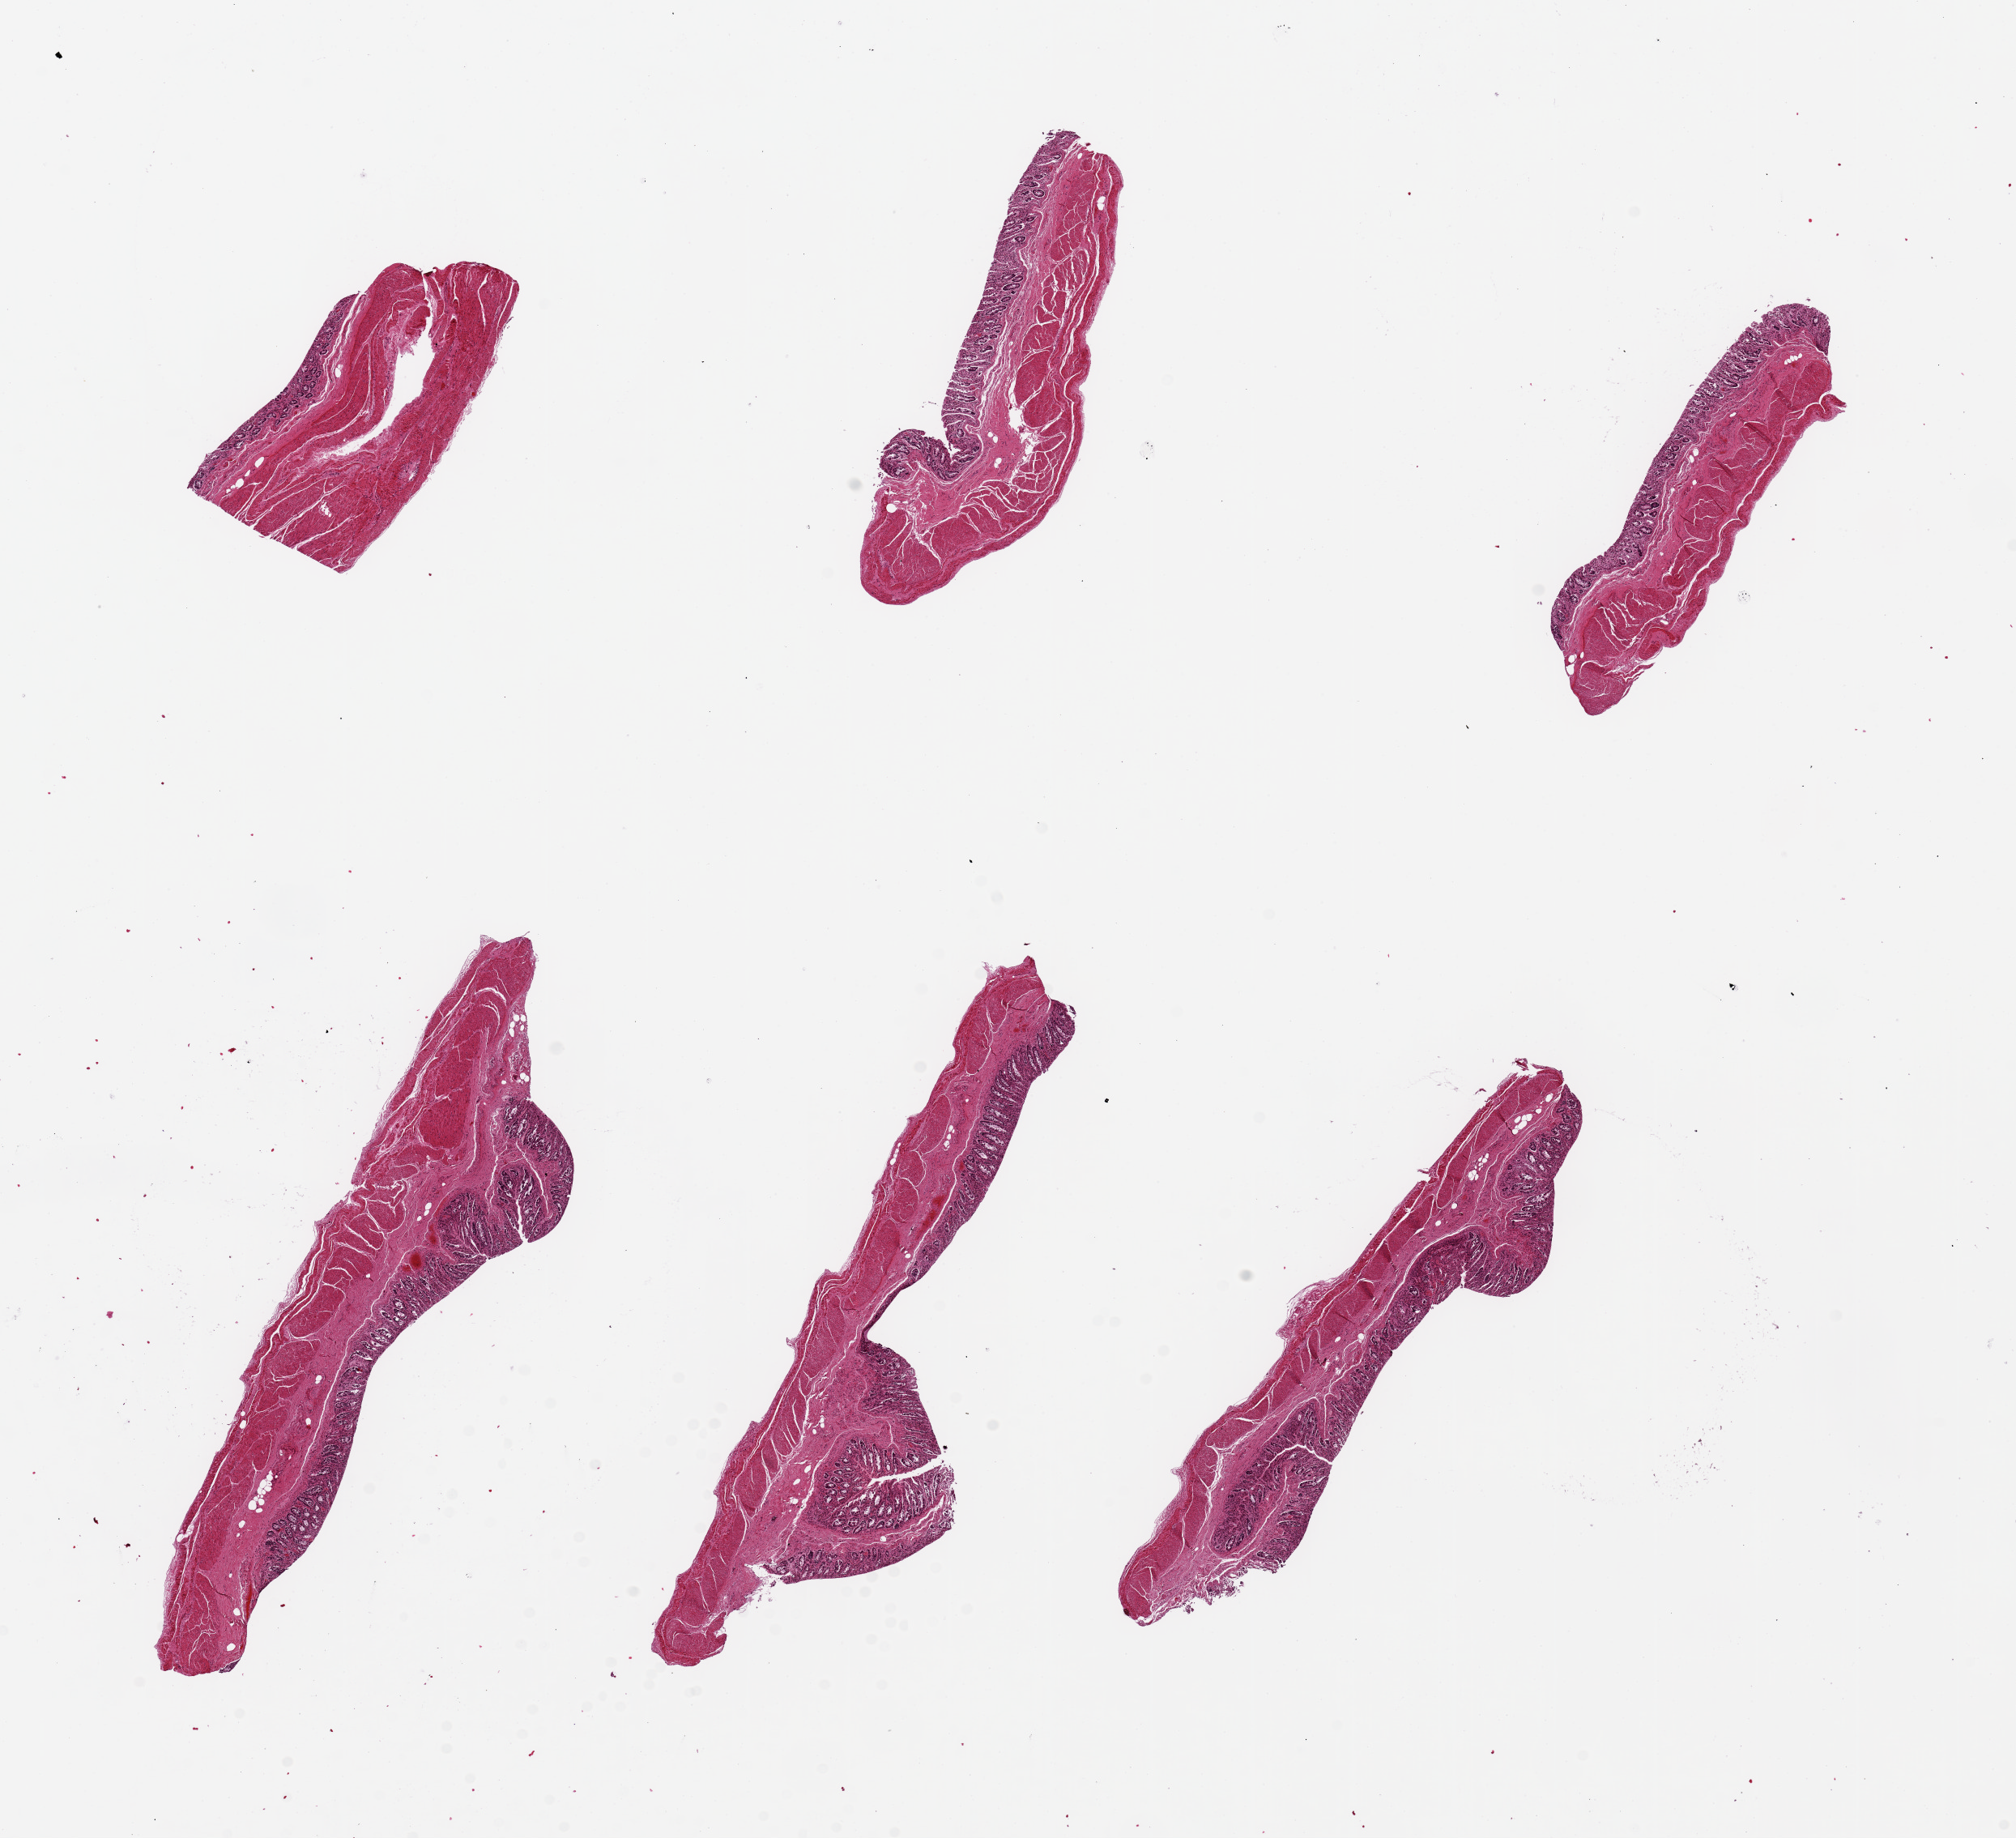
Digitized haematoxylin and eosin-stained section, brightfield — low-resolution overview of the scanned area, about 19.7 x 17.9 mm (slide scanned at 20x), PAXgene-fixed, paraffin-embedded tissue, target tissue: transverse colon, tissue donor sample. Donor: male.
- review note (as recorded): 6 pieces, up to 8x2mm; Well sampled mucosa (3) and muscle (2)